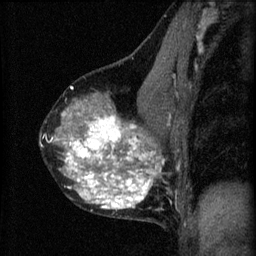
Breast MRI (dynamic contrast-enhanced), one sagittal slice; position 36 of 60 along the scan axis; 3 images stored at this slice position (order not interpretable as contrast timing); 1.5 T; TE 4.2 ms, TR 8.2 ms; 2 mm slice thickness; 256 × 256 image matrix, field of view 180 × 180 mm. Female patient, age 40 years.
Structures marked on this image (semi-automatically segmented with operator editing):
- analysis volume of interest (the breast-tissue region the enhancement analysis was run in; not a lesion): bounding box (x1, y1, x2, y2) in pixels: (40, 76, 179, 219)
- tumour enhancement mask (voxels above the 70 % enhancement threshold inside the analysis volume of interest): (42, 108, 179, 209)